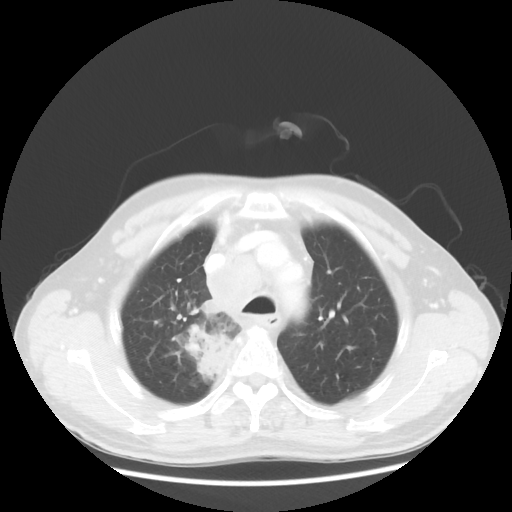
Chest CT, one axial slice. Position 95 of 124 along the scan axis. Reconstruction kernel STANDARD. 100 kVp. Lung window (W 1500 / L -600 HU). 5 mm slice thickness. 512 × 512 image matrix. Male patient, age 64 years. Case-level facts recorded for this patient, not image findings: clinical TNM (as recorded): T3 N3 M0; histopathological grade: G3.
Structures marked on this image (bounding box drawn by a radiologist):
- lung tumour (recorded histology: small cell carcinoma): box from (x=181, y=316) to (x=242, y=391) px